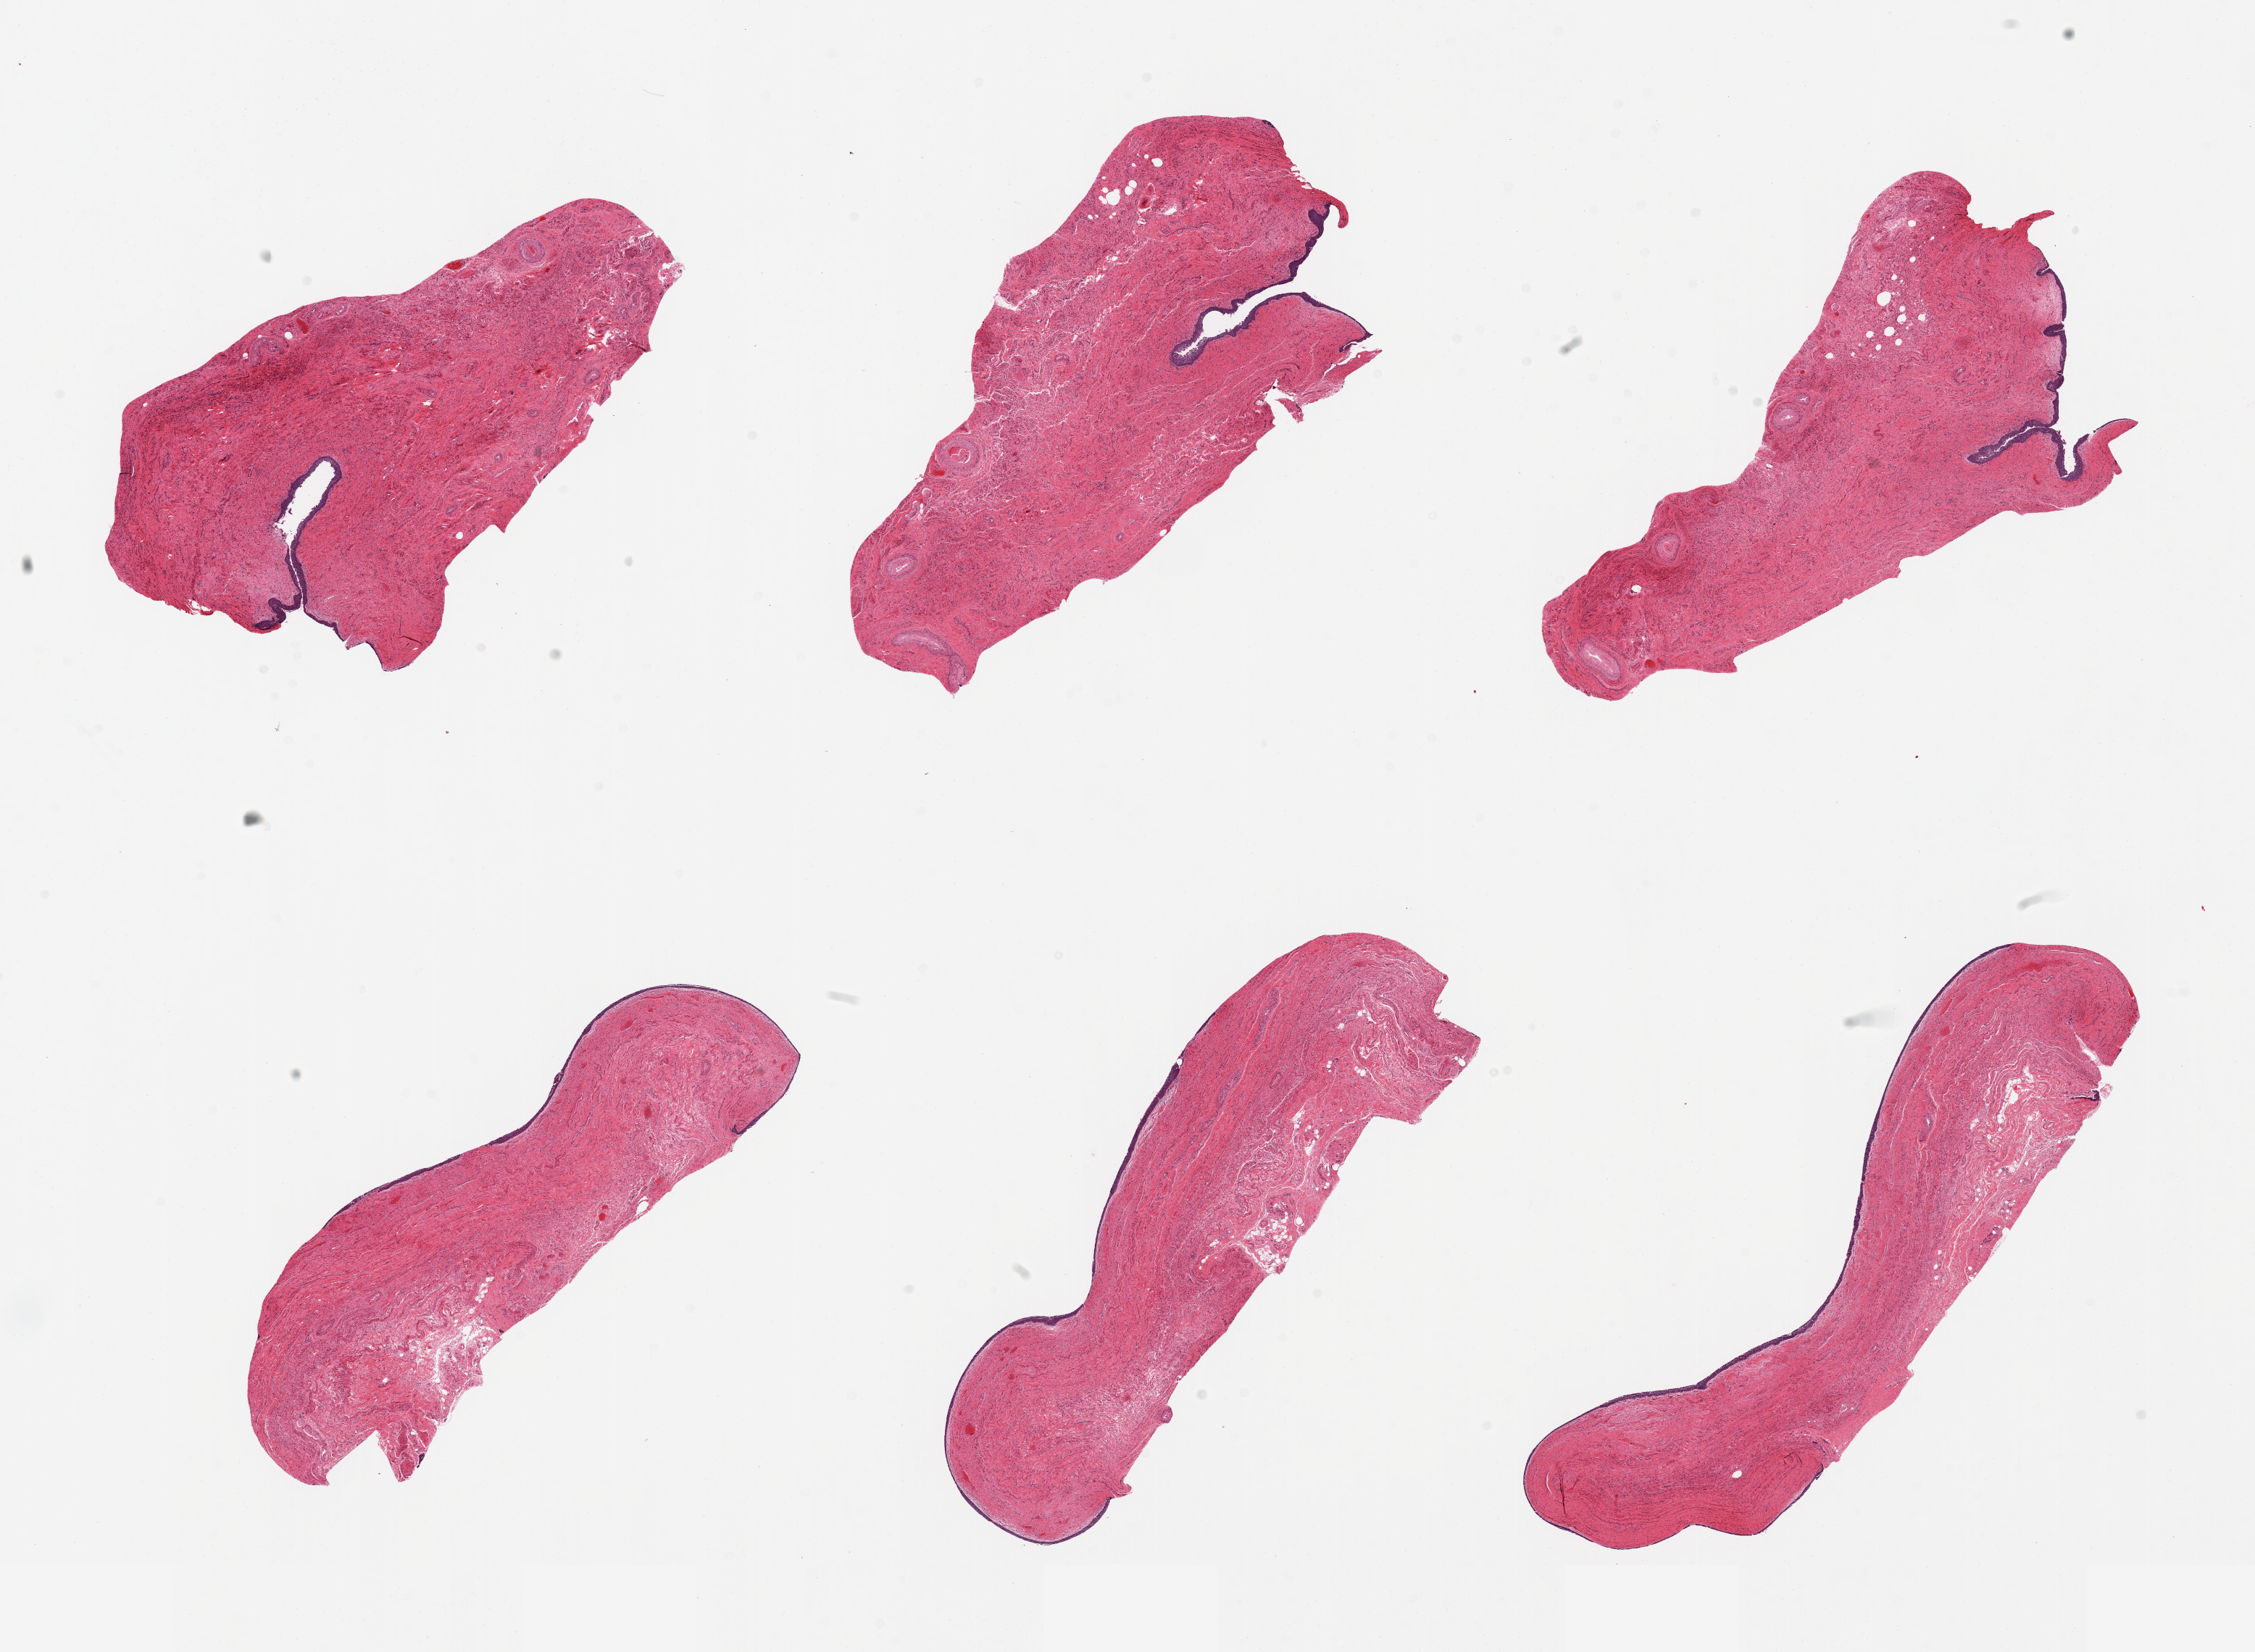
Whole-slide image, H&E stain, brightfield, low-resolution overview of the scanned area, about 24.6 x 18.0 mm (acquisition: 20x scan), PAXgene-fixed, paraffin-embedded tissue, target tissue: vagina, donor tissue sample.
* review note (as recorded): 6 pieces; atrophic, partly sloughed epithelium